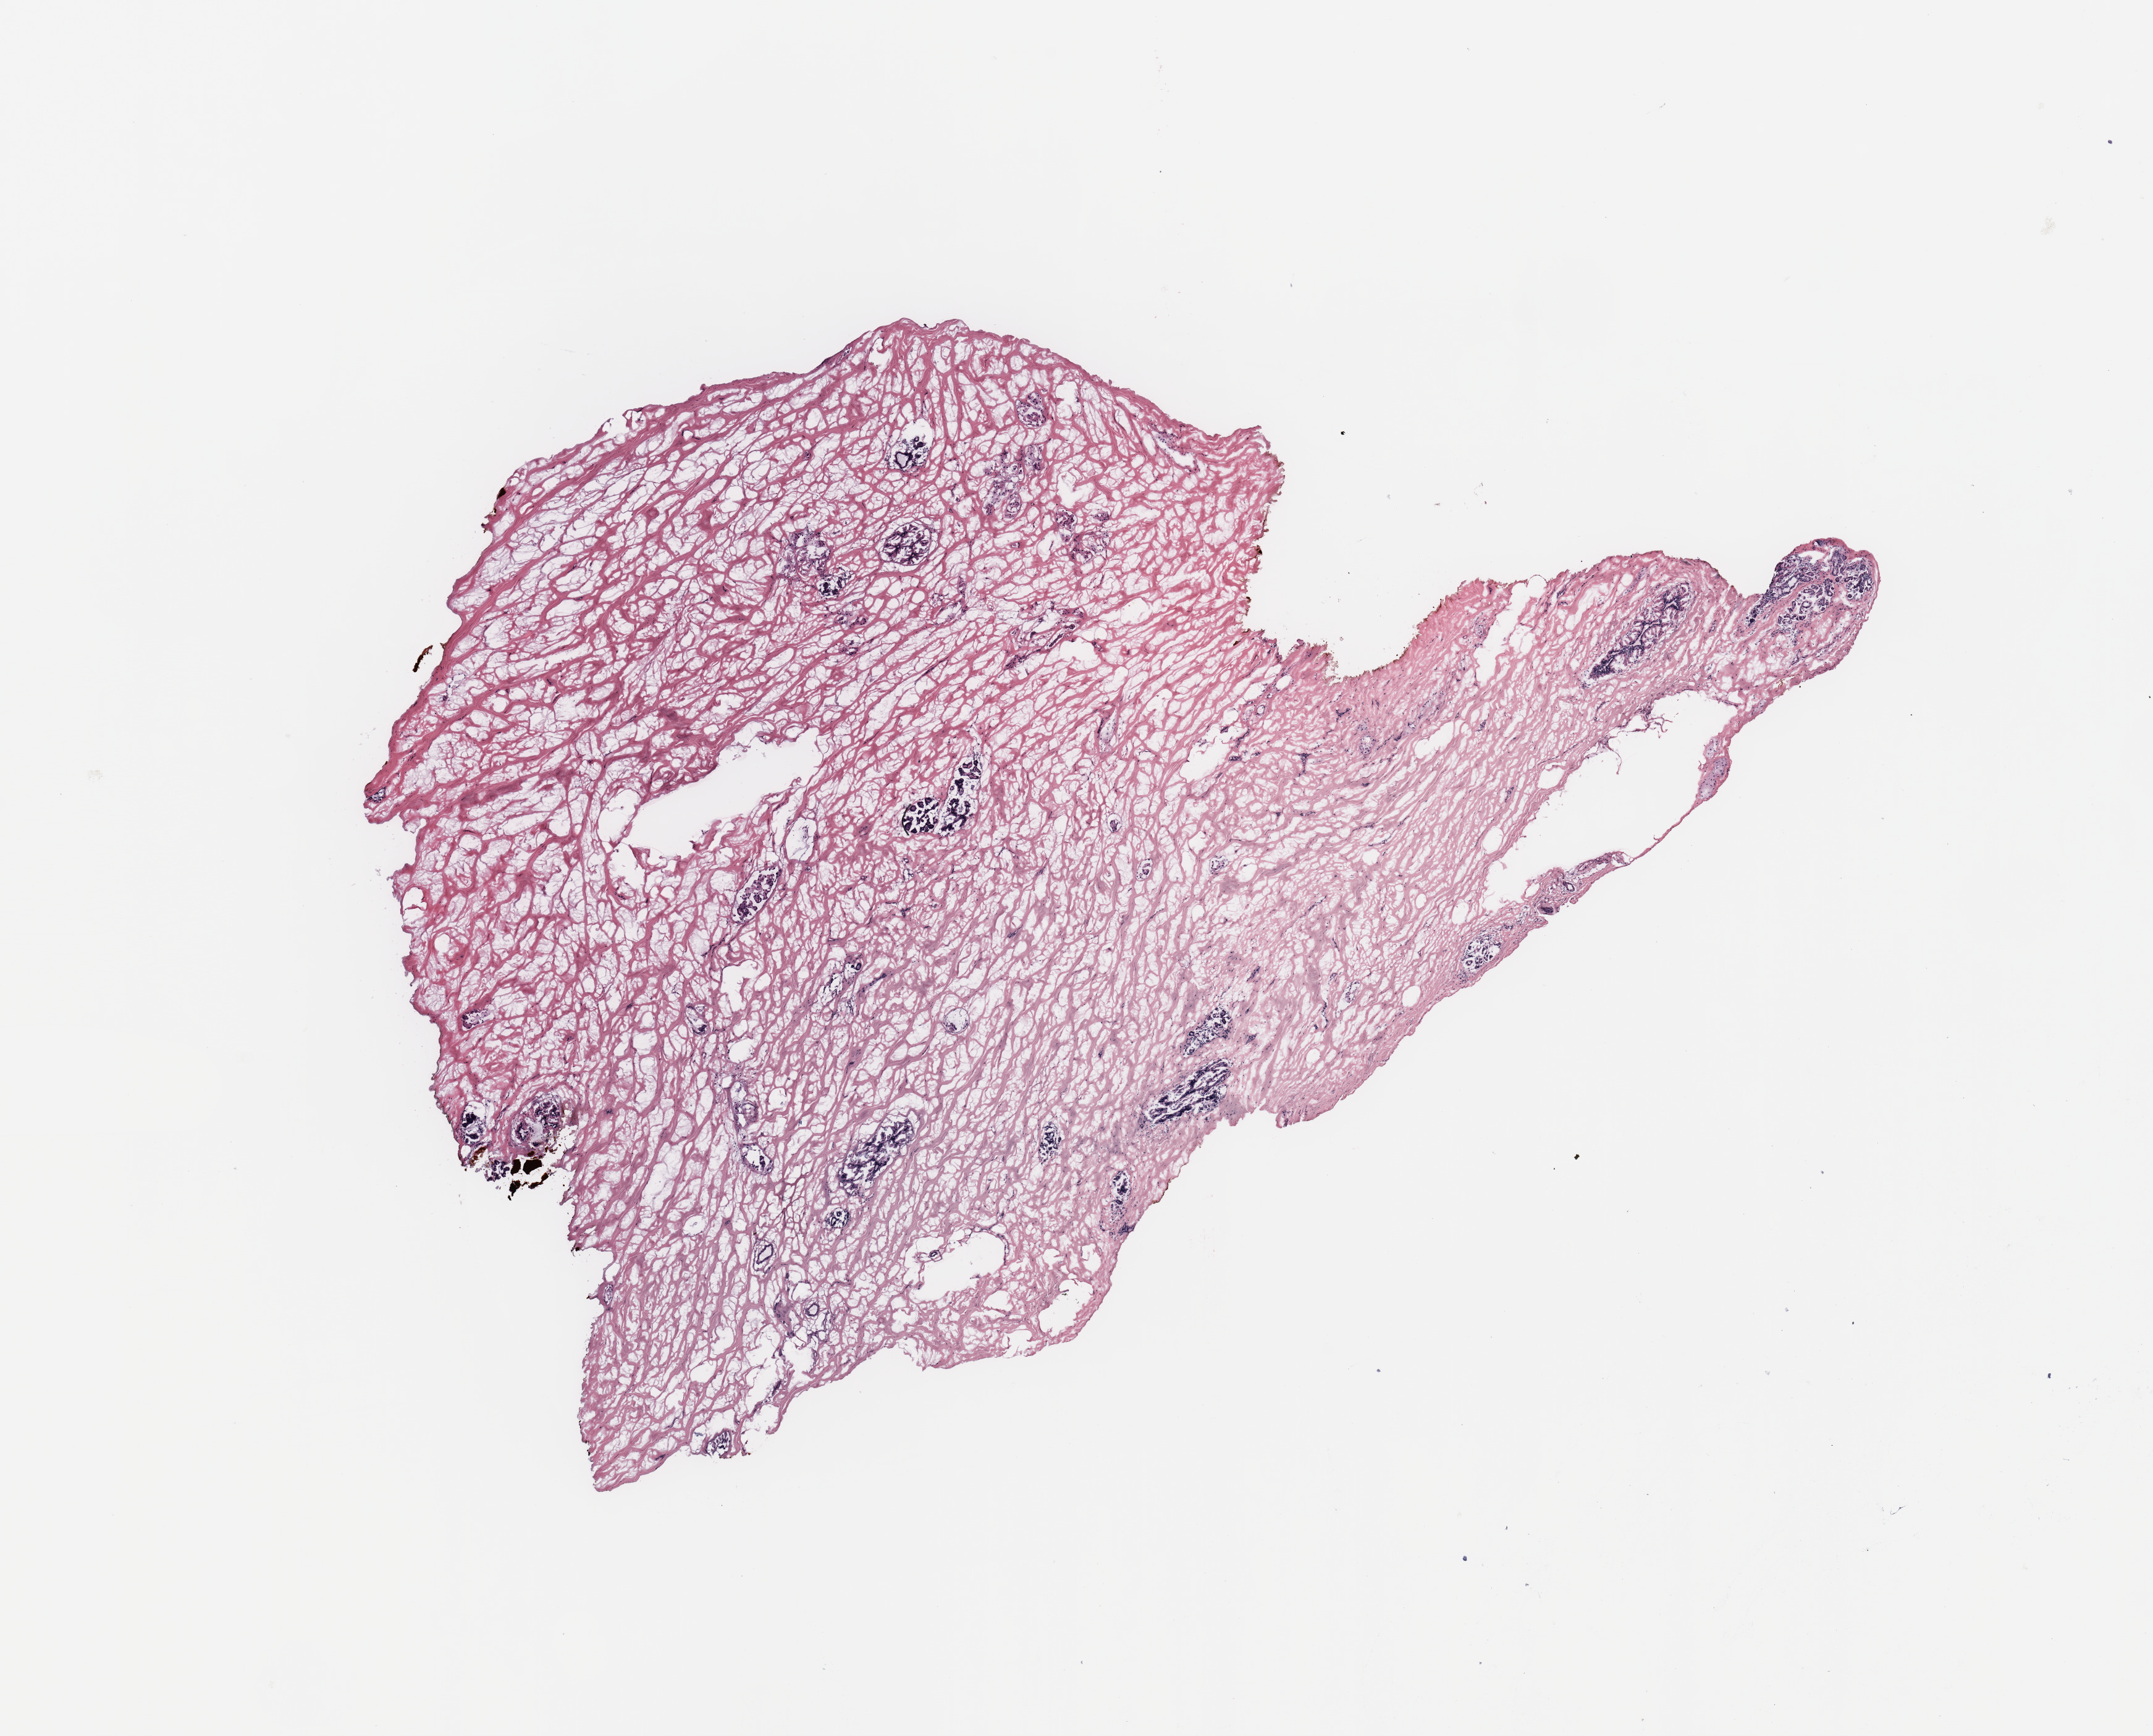
Digitized H&E tissue section (whole slide) — low-resolution overview of the scanned area, about 13.8 x 11.1 mm (slide scanned at 20x); breast, tissue type not recorded.
* patient diagnosis (cohort enrolment): breast cancer (breast)